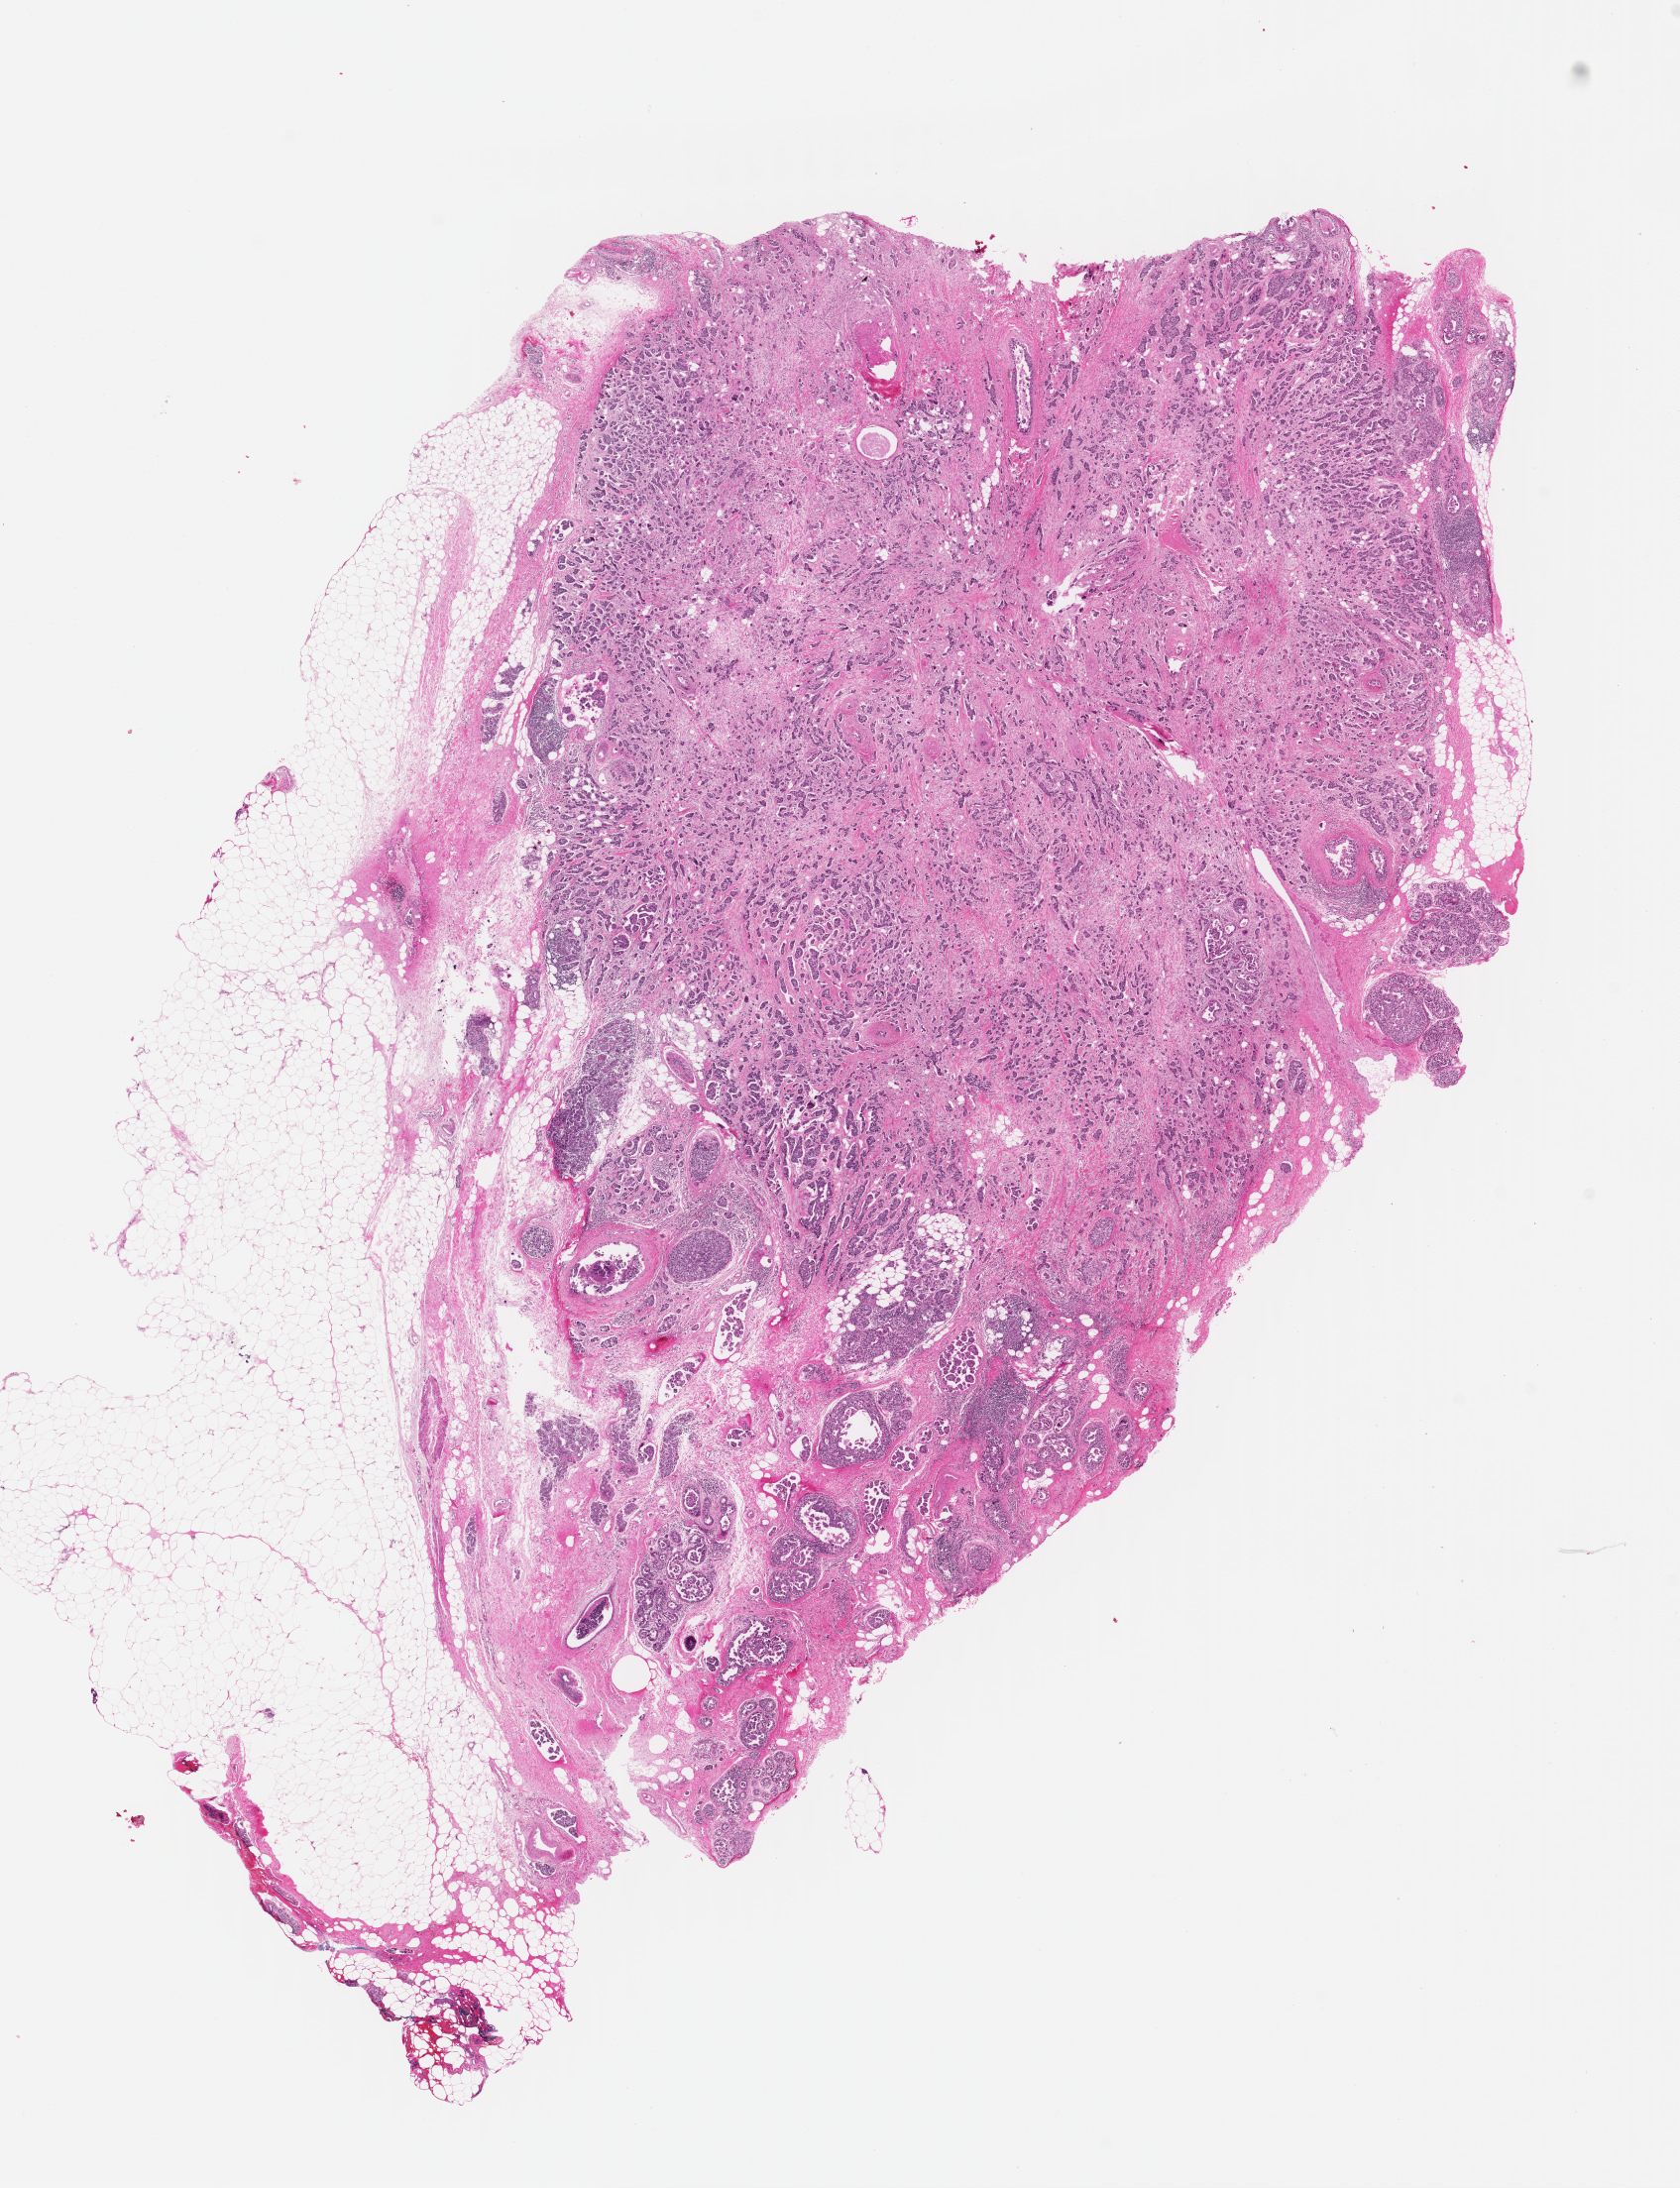
H&E-stained whole-slide image, shown as a low-resolution overview of the whole scanned area (about 13.3 x 17.4 mm, from a 40x scan). FFPE section. Breast, primary tumour sample. Female patient; age at initial diagnosis 62 years.
* AJCC pathologic stage: IIIA (6th edition)
* laterality: left
* lymph nodes positive (case pathology): 9 of 19 examined
* histologic diagnosis: Infiltrating duct carcinoma, NOS